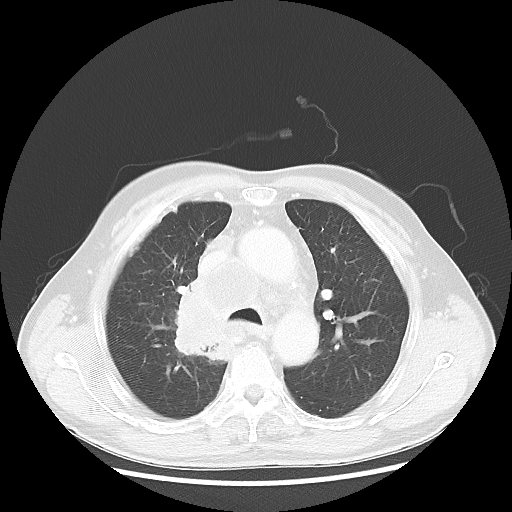
Chest CT, one axial slice; position 39 of 60 along the scan axis; reconstruction kernel LUNG; 100 kVp; lung window (W 1500 / L -600 HU); 5 mm slice thickness; 512 × 512 image matrix, field of view 382 × 382 mm. Patient: male, 64 years. From the clinical record (not read from this slice): clinical TNM (as recorded): T3 N3 M0.
Annotated regions visible in this slice (bounding box drawn by a radiologist):
- lung tumour (recorded histology: small cell carcinoma): bounding box <161,282,227,370> (left, top, right, bottom; pixels)